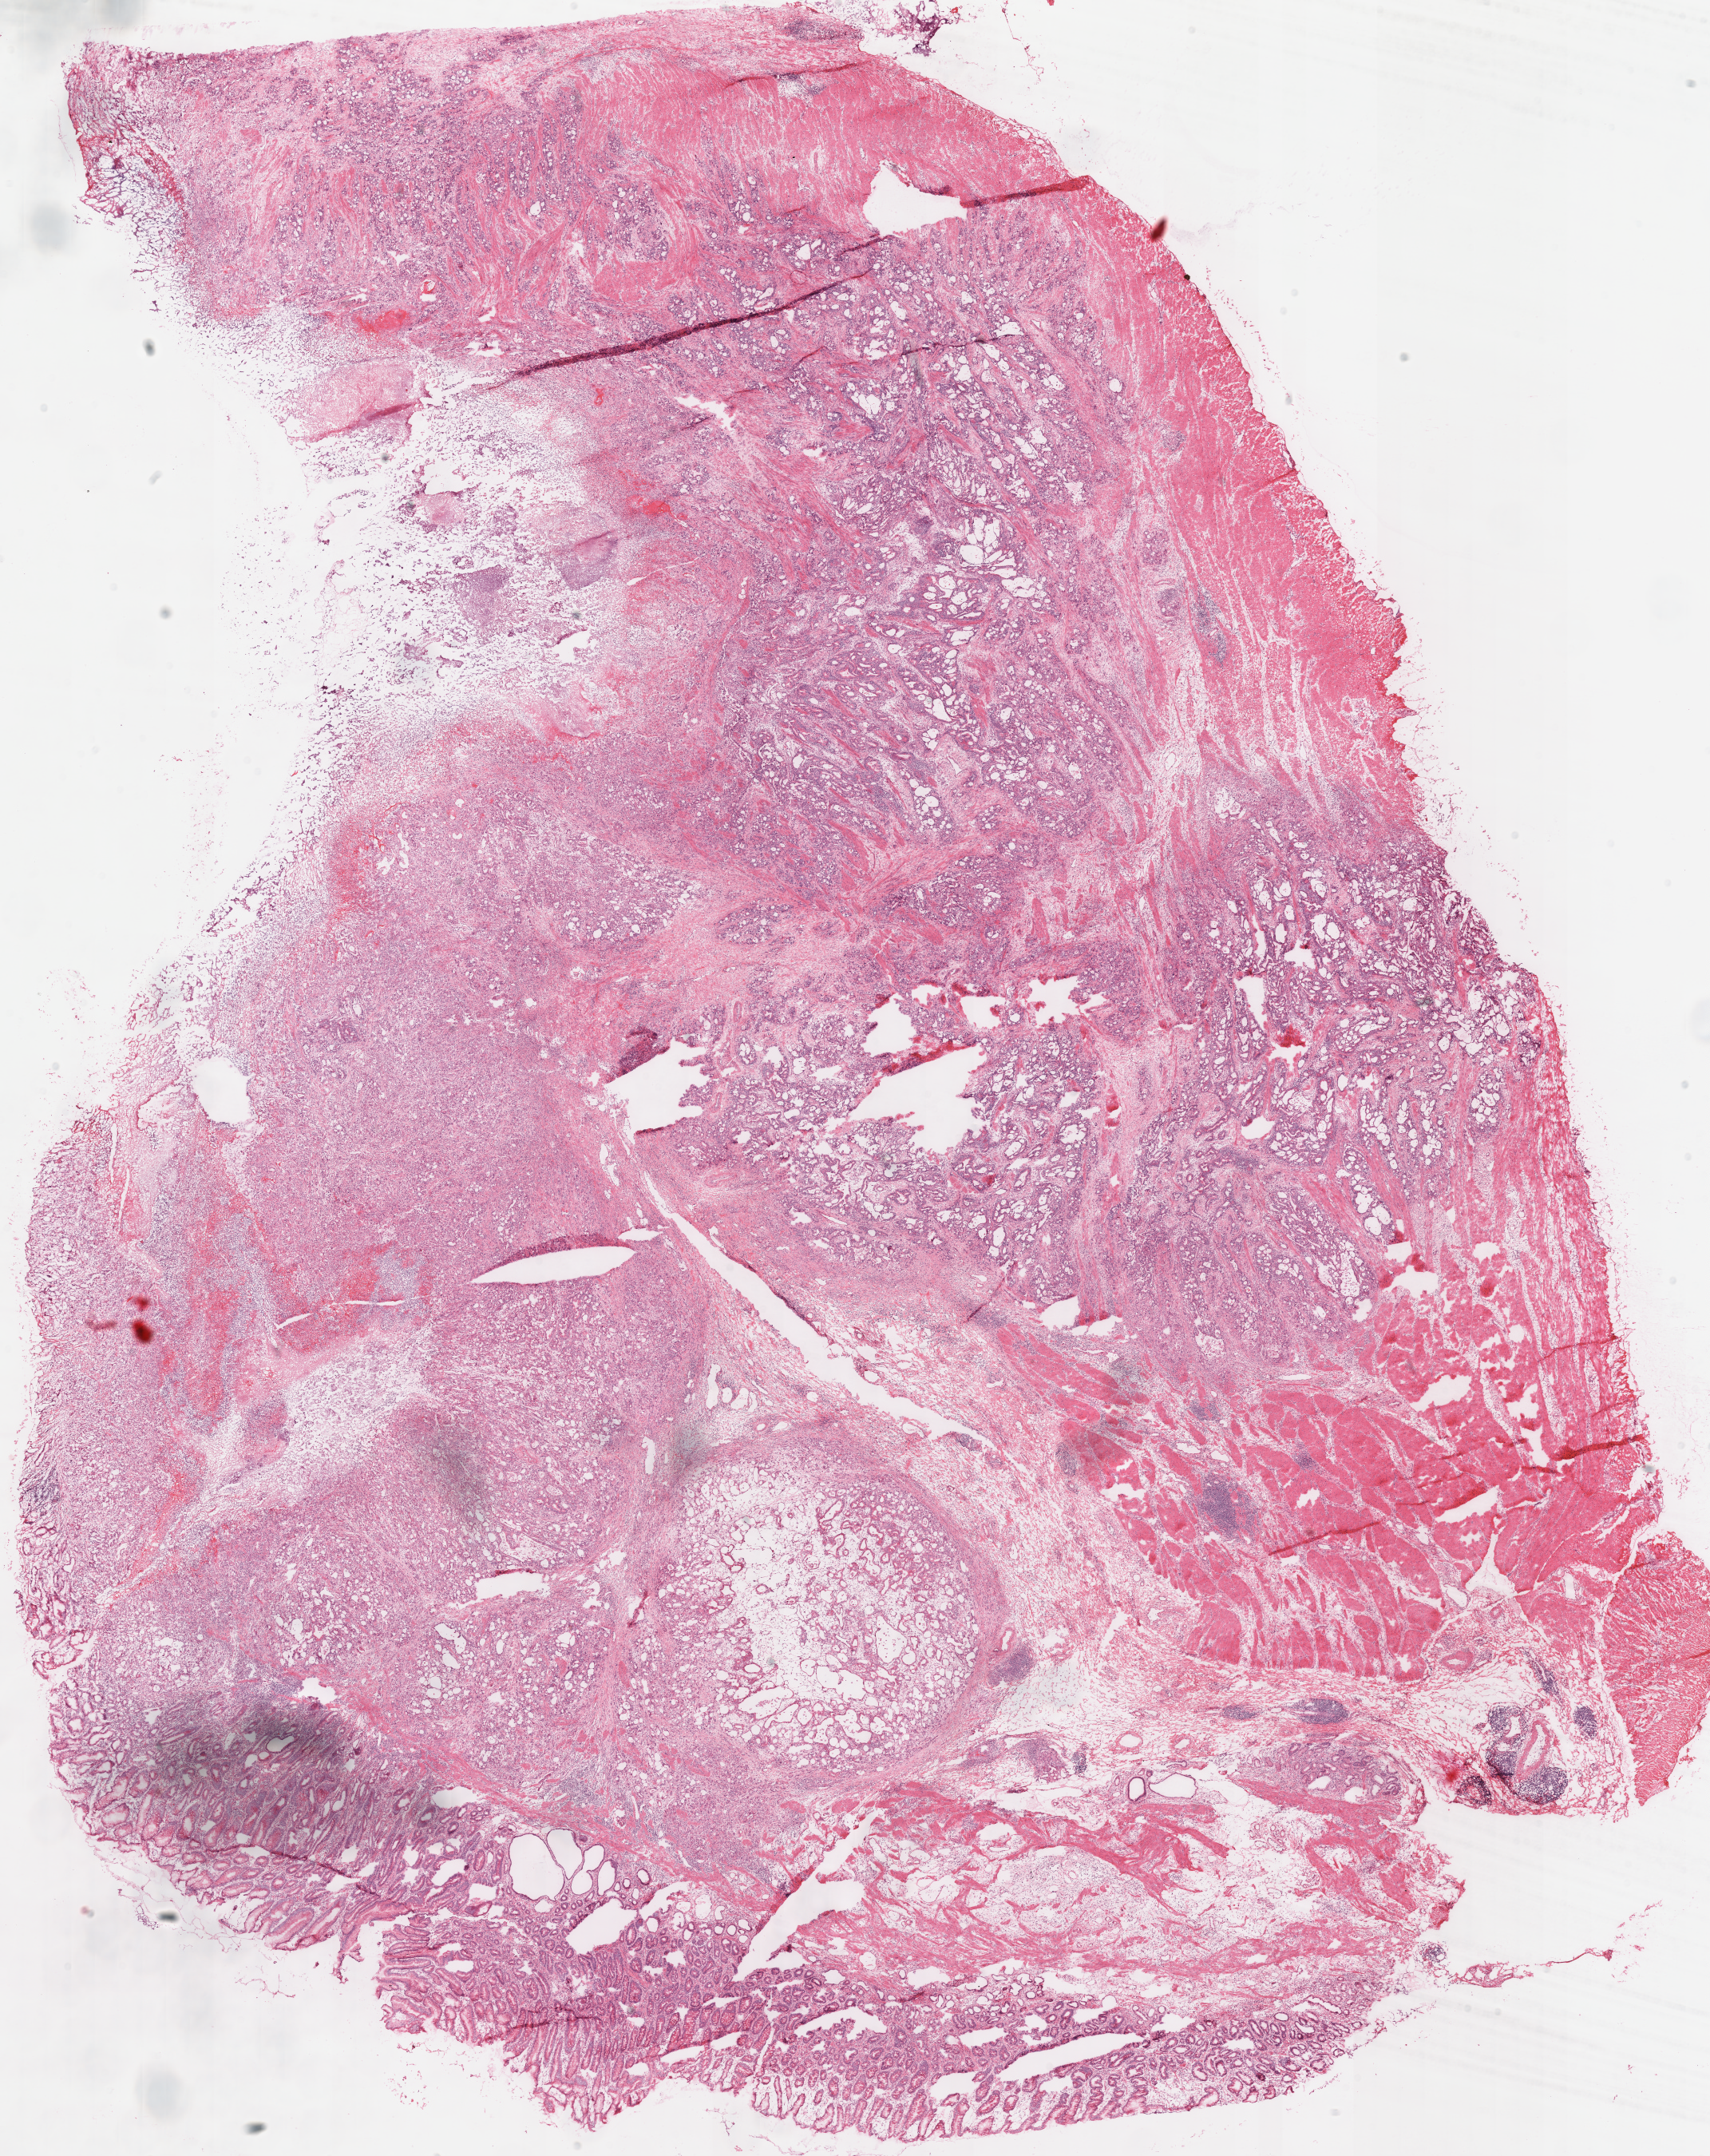
Digitized H&E-stained tissue section (whole slide) — shown as a low-resolution overview of the whole scanned area (about 16.9 x 21.3 mm, acquisition: 40x scan); frozen section from the top of the tissue portion; primary tumour sample from the stomach. Patient: male, age at initial diagnosis 75 years. Histologic grade: G3 (poorly differentiated). Composition of this section per pathologist review: tumour cells 72%, tumour nuclei 63%, normal cells 28%, stromal cells 0%, necrosis 0%. Inflammatory infiltration, as recorded: lymphocyte infiltration 10%, monocyte infiltration 2%, neutrophil infiltration 2%.
AJCC pathologic stage: IIIB. Pathologic diagnosis: Tubular adenocarcinoma (gastric antrum). Lymph nodes positive (case pathology): 3 of 5 examined.